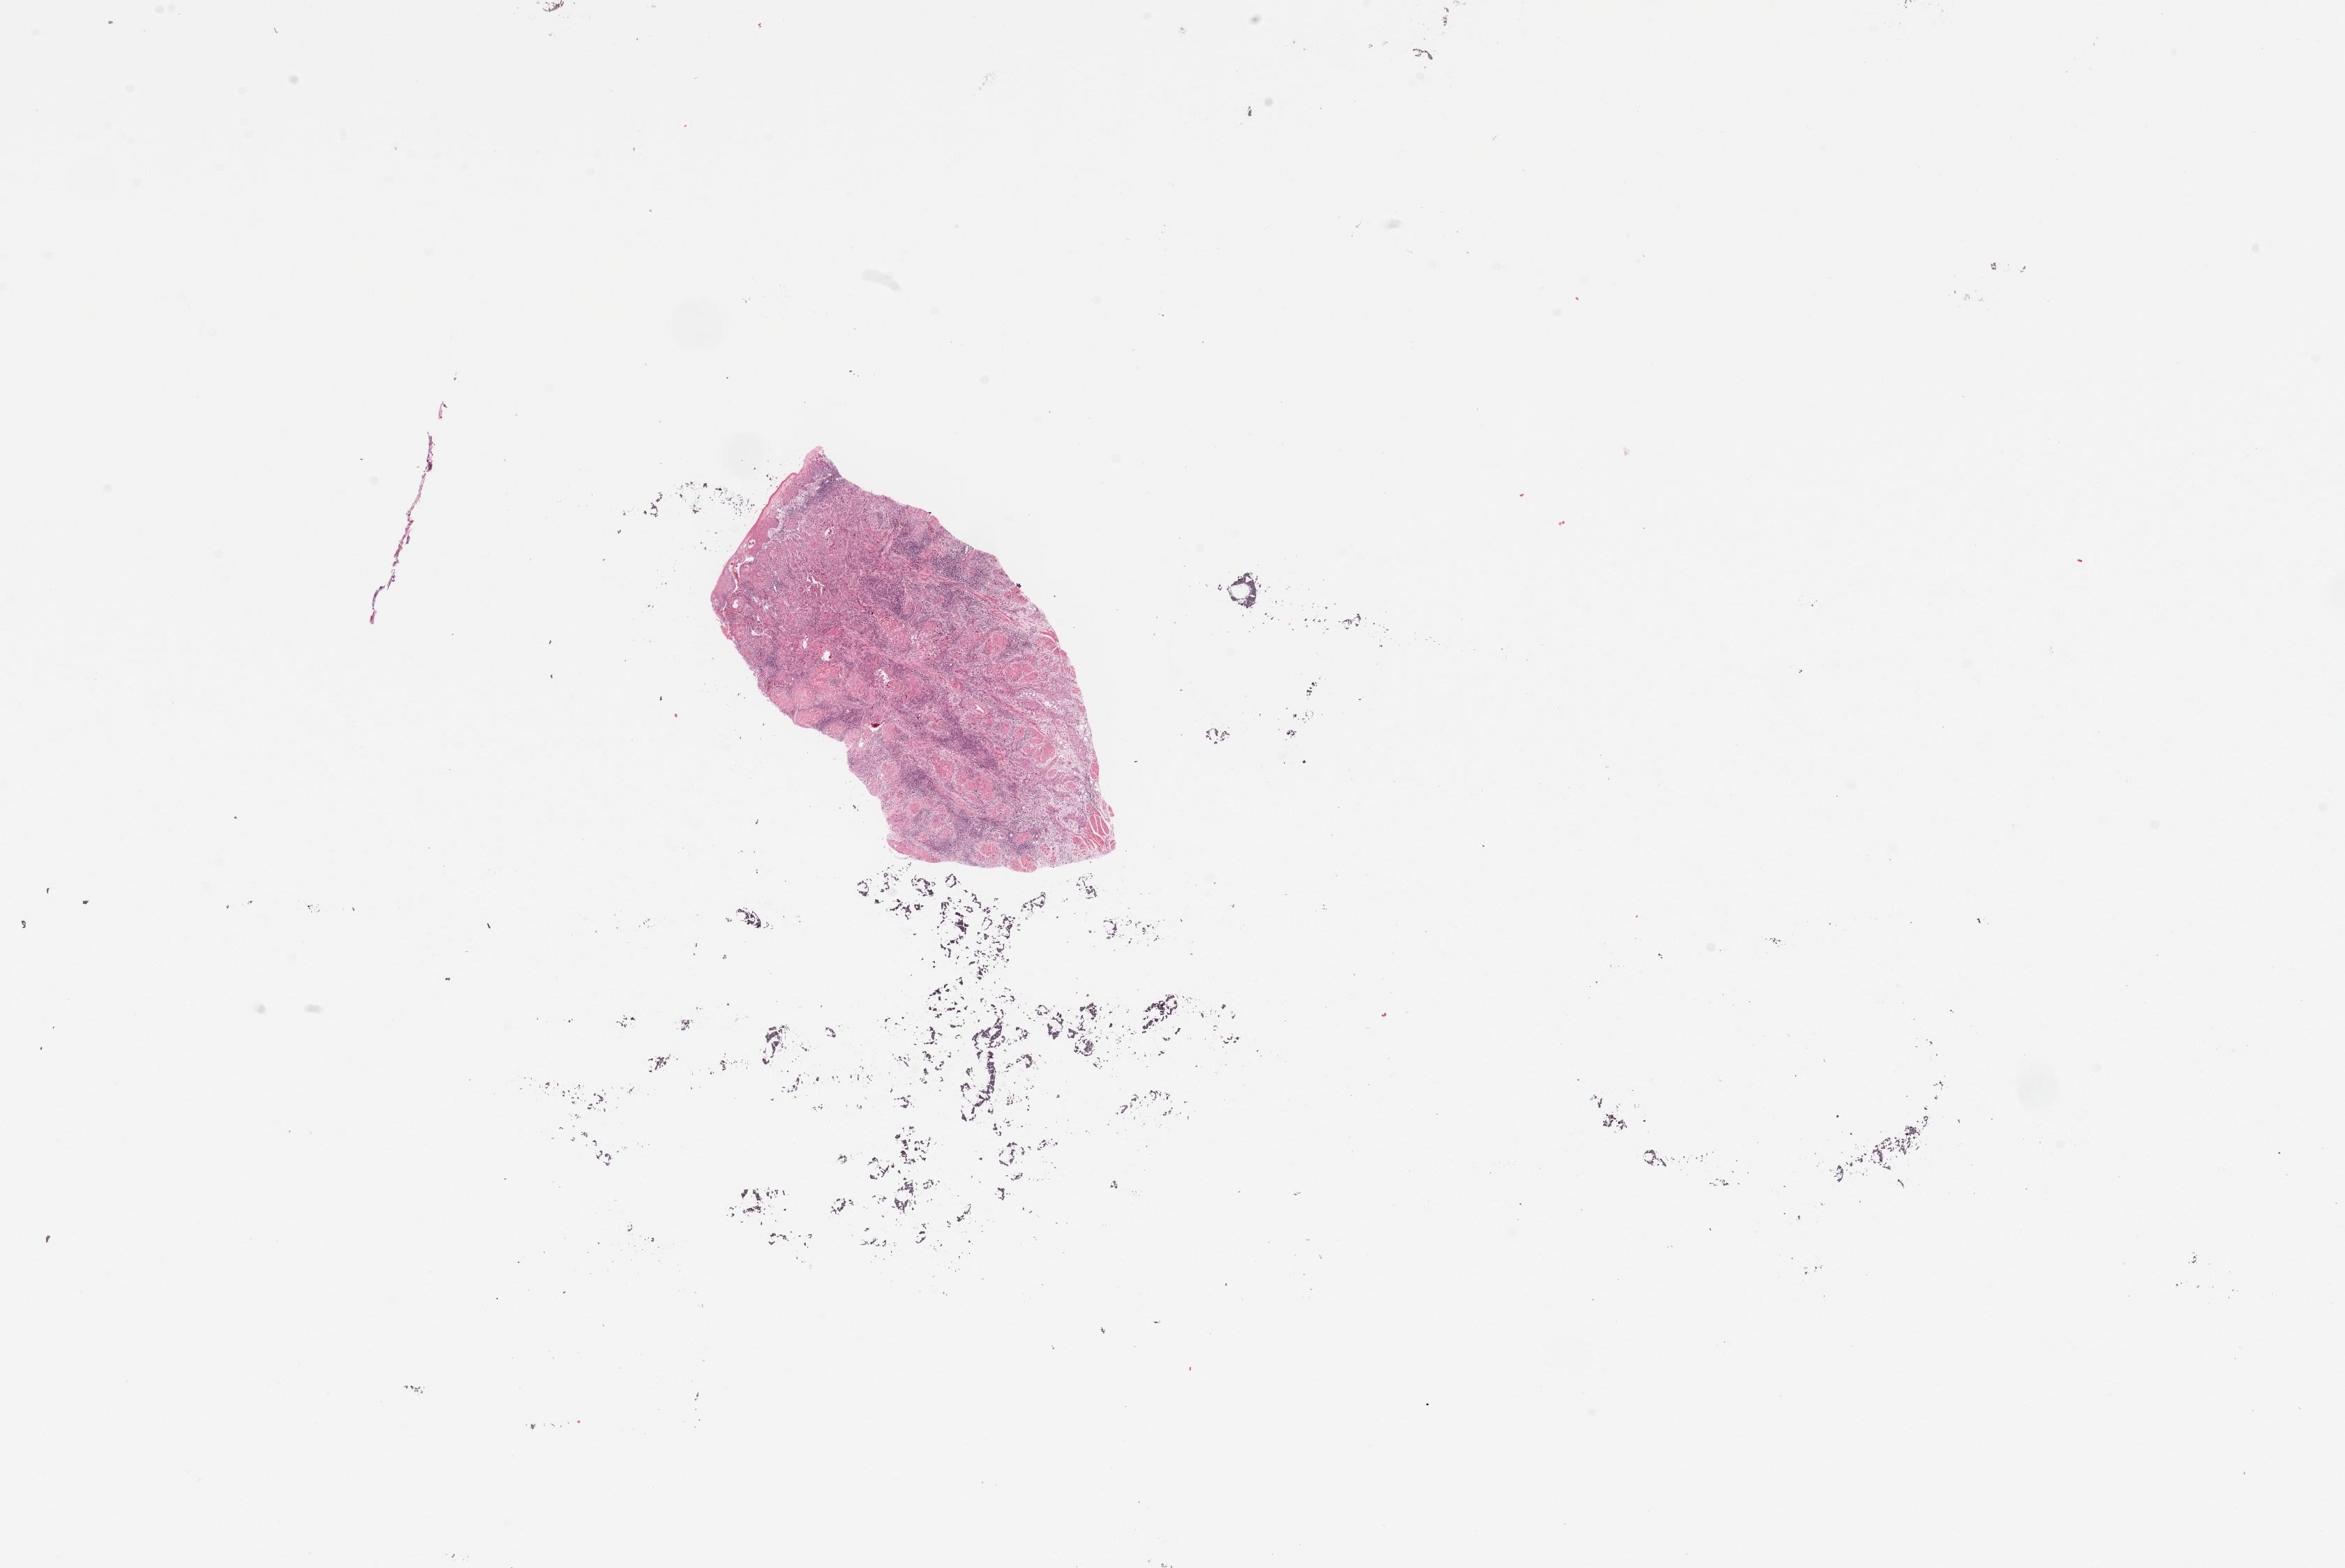
Whole-slide histology image, H&E-stained — low-resolution overview of the scanned area, about 26.6 x 17.8 mm (slide scanned at 20x), tumour tissue sample, sampled site: tongue. Male, 40 y/o. Histologic grade: G2 (moderately differentiated). Slide review estimates, as recorded: tumour nuclei 80%, necrosis 3%.
Histologic diagnosis: Squamous cell carcinoma, NOS (tongue, NOS). AJCC pathologic stage: III. Primary tumour site (as recorded): oral cavity.